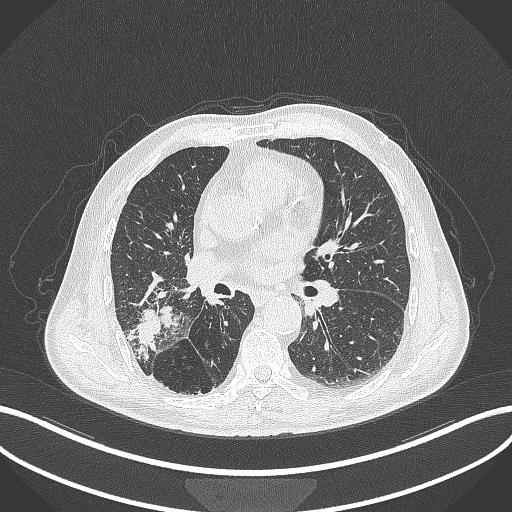
Chest CT, one axial slice. Slice 217 of 429 in the series (ordered by position). Reconstruction kernel B70f. 120 kVp. Lung window (W 1500 / L -600 HU). 1 mm slice thickness. 512 × 512 image matrix, field of view 400 × 400 mm. Patient: male, 72 years. Case-level facts recorded for this patient, not image findings: clinical TNM (as recorded): T3 N2 M0.
Outlined on this slice (bounding box drawn by a radiologist):
- lung tumour (recorded histology: adenocarcinoma): bounding box (x1, y1, x2, y2) in pixels: (130, 304, 180, 356)